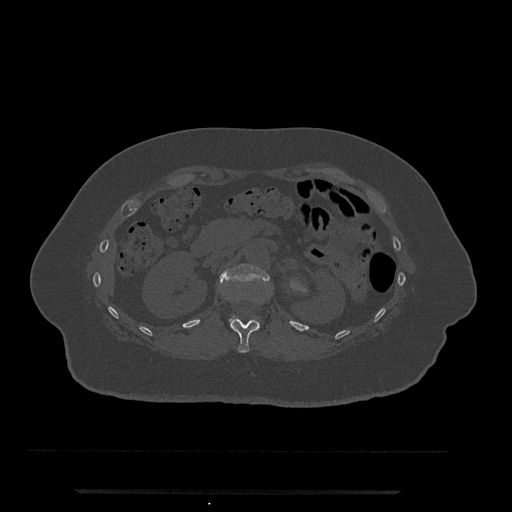
CT including the spine, one axial slice; reconstruction kernel Br40s/3; bone window (W 1800 / L 400 HU); 0.5 mm slice thickness; 512 × 512 image matrix. Female patient, age 51 years. From the clinical record (not read from this slice): primary cancer: neuro; vertebrae with lytic lesions (as recorded): T8.
Annotated regions visible in this slice (semi-automatic segmentation, software-assisted and operator-edited):
- L1 vertebra: bounding box <220,264,270,326> (left, top, right, bottom; pixels)
- T12 vertebra: <230,318,259,353>